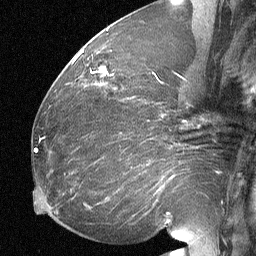
Breast MRI (dynamic contrast-enhanced), one sagittal slice; slice 31 of 64 in the series (ordered by position); dynamic contrast-enhanced study with each time point stored as its own series, time point 2 of 3 at this slice position (early post-contrast, ordered by acquisition time); 1.5 T; TE 4.8 ms, TR 27 ms; 256 × 256 image matrix, field of view 200 × 200 mm. Patient: female, 60 years. Case-level facts recorded for this patient, not image findings: setting: breast cancer imaged before/during neoadjuvant chemotherapy; receptor status: HR-positive, HER2-negative.
Outlined on this slice (semi-automatic segmentation, software-assisted and operator-edited):
- analysis volume of interest (the breast-tissue region the enhancement analysis was run in; not a lesion): bounding box <92,62,134,102> (left, top, right, bottom; pixels)
- tumour enhancement mask (voxels above the 90 % enhancement threshold inside the analysis volume of interest): <101,68,104,72>